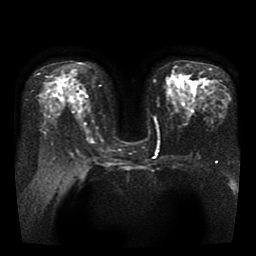
Breast MRI, one axial slice. Position 21 of 41 along the scan axis. Diffusion-weighted series; image 2 of 4 stored at this slice position (different b-values; order by instance number). 1.5 T. 5 mm slice thickness. 256 × 256 image matrix, field of view 330 × 330 mm. Female patient.
Annotated regions visible in this slice (manually delineated by an expert):
- tumour on diffusion-weighted imaging: bounding box (x1, y1, x2, y2) in pixels: (174, 87, 182, 95)